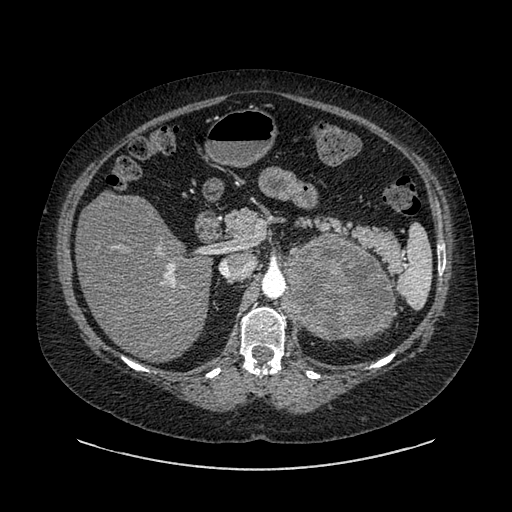
Contrast-enhanced abdominal CT, one axial slice. Position 567 of 769 along the scan axis. Reconstruction kernel SOFT. 120 kVp. Intravenous contrast given. Soft-tissue window (W 400 / L 40 HU). 0.62 mm slice thickness. 512 × 512 image matrix. Patient: female, 61 years. Case-level facts recorded for this patient, not image findings: diagnosis: adrenocortical carcinoma; tumour side: left adrenal.
Annotated regions visible in this slice (semi-automatic segmentation, software-assisted and operator-edited):
- mass: bounding box [x1, y1, x2, y2] px = [284, 234, 391, 340]